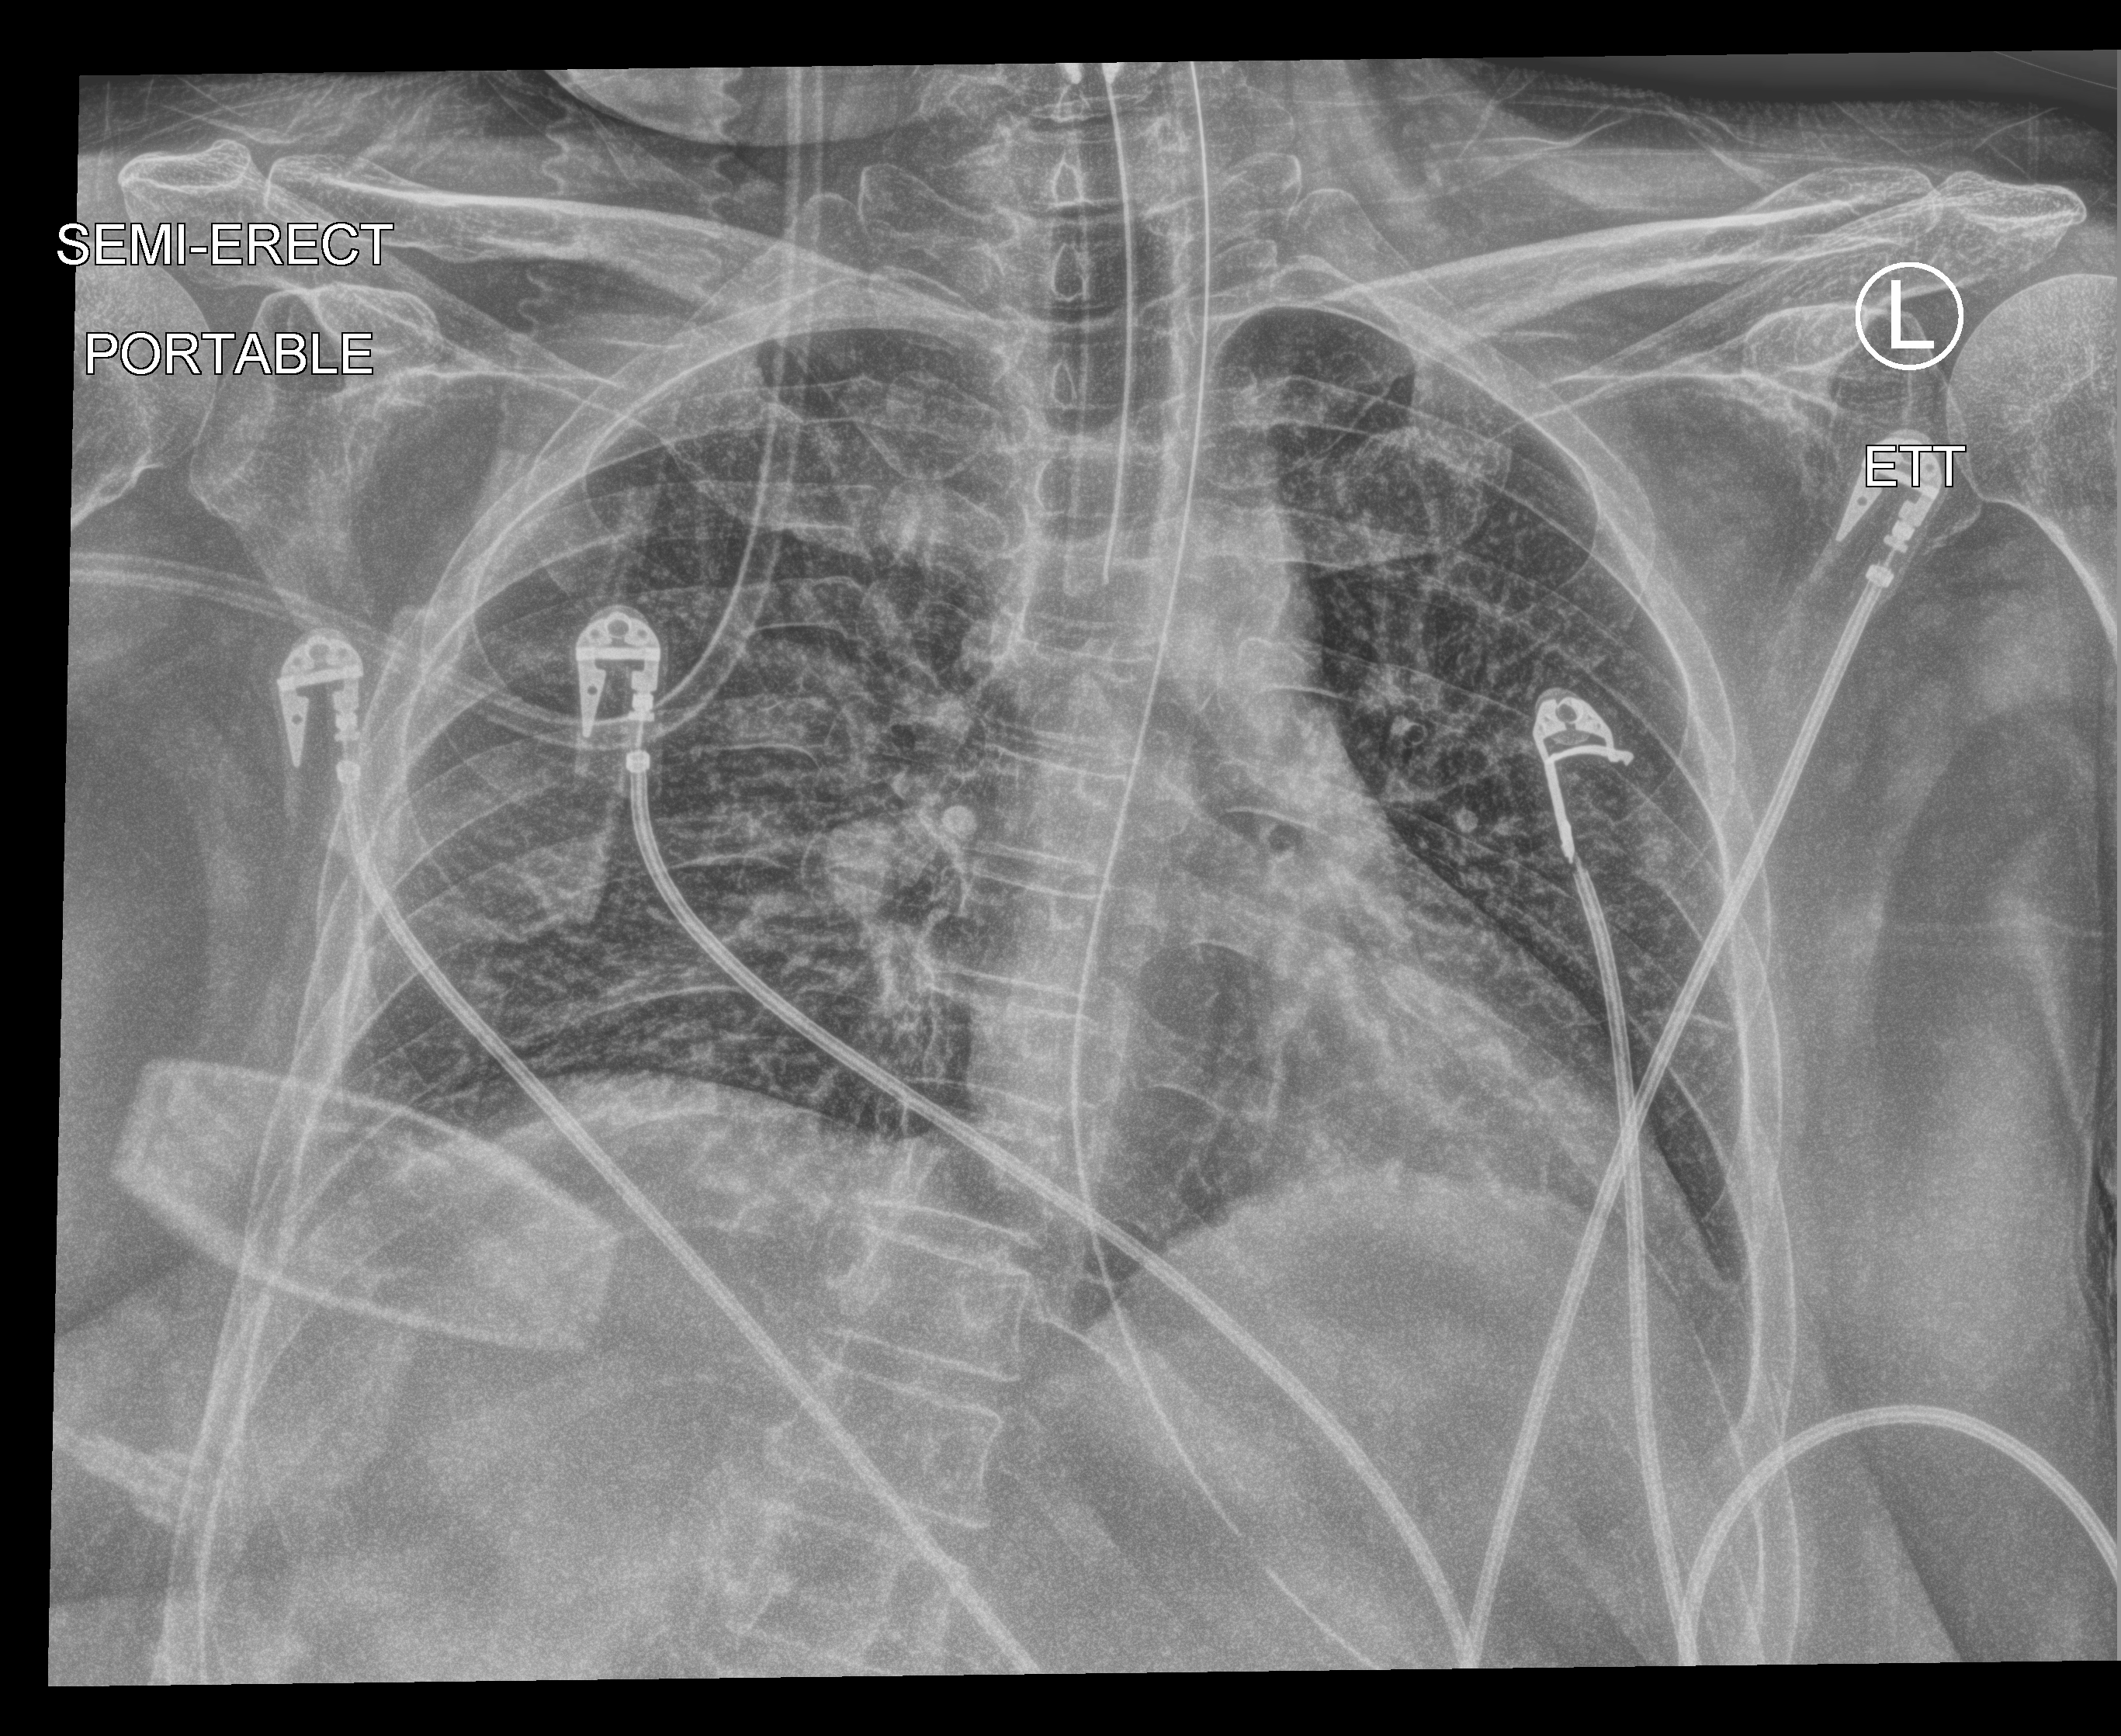
Chest X-ray (portable), anteroposterior (AP) projection. Female patient hospitalised with COVID-19, age 18–59 years.
From the hospital-stay record, not from the radiograph (when in the stay this image was taken is not recorded):
- length of hospital stay: 44 days
- admitted to intensive care during this hospital stay: yes
- mechanically ventilated during this hospital stay: no